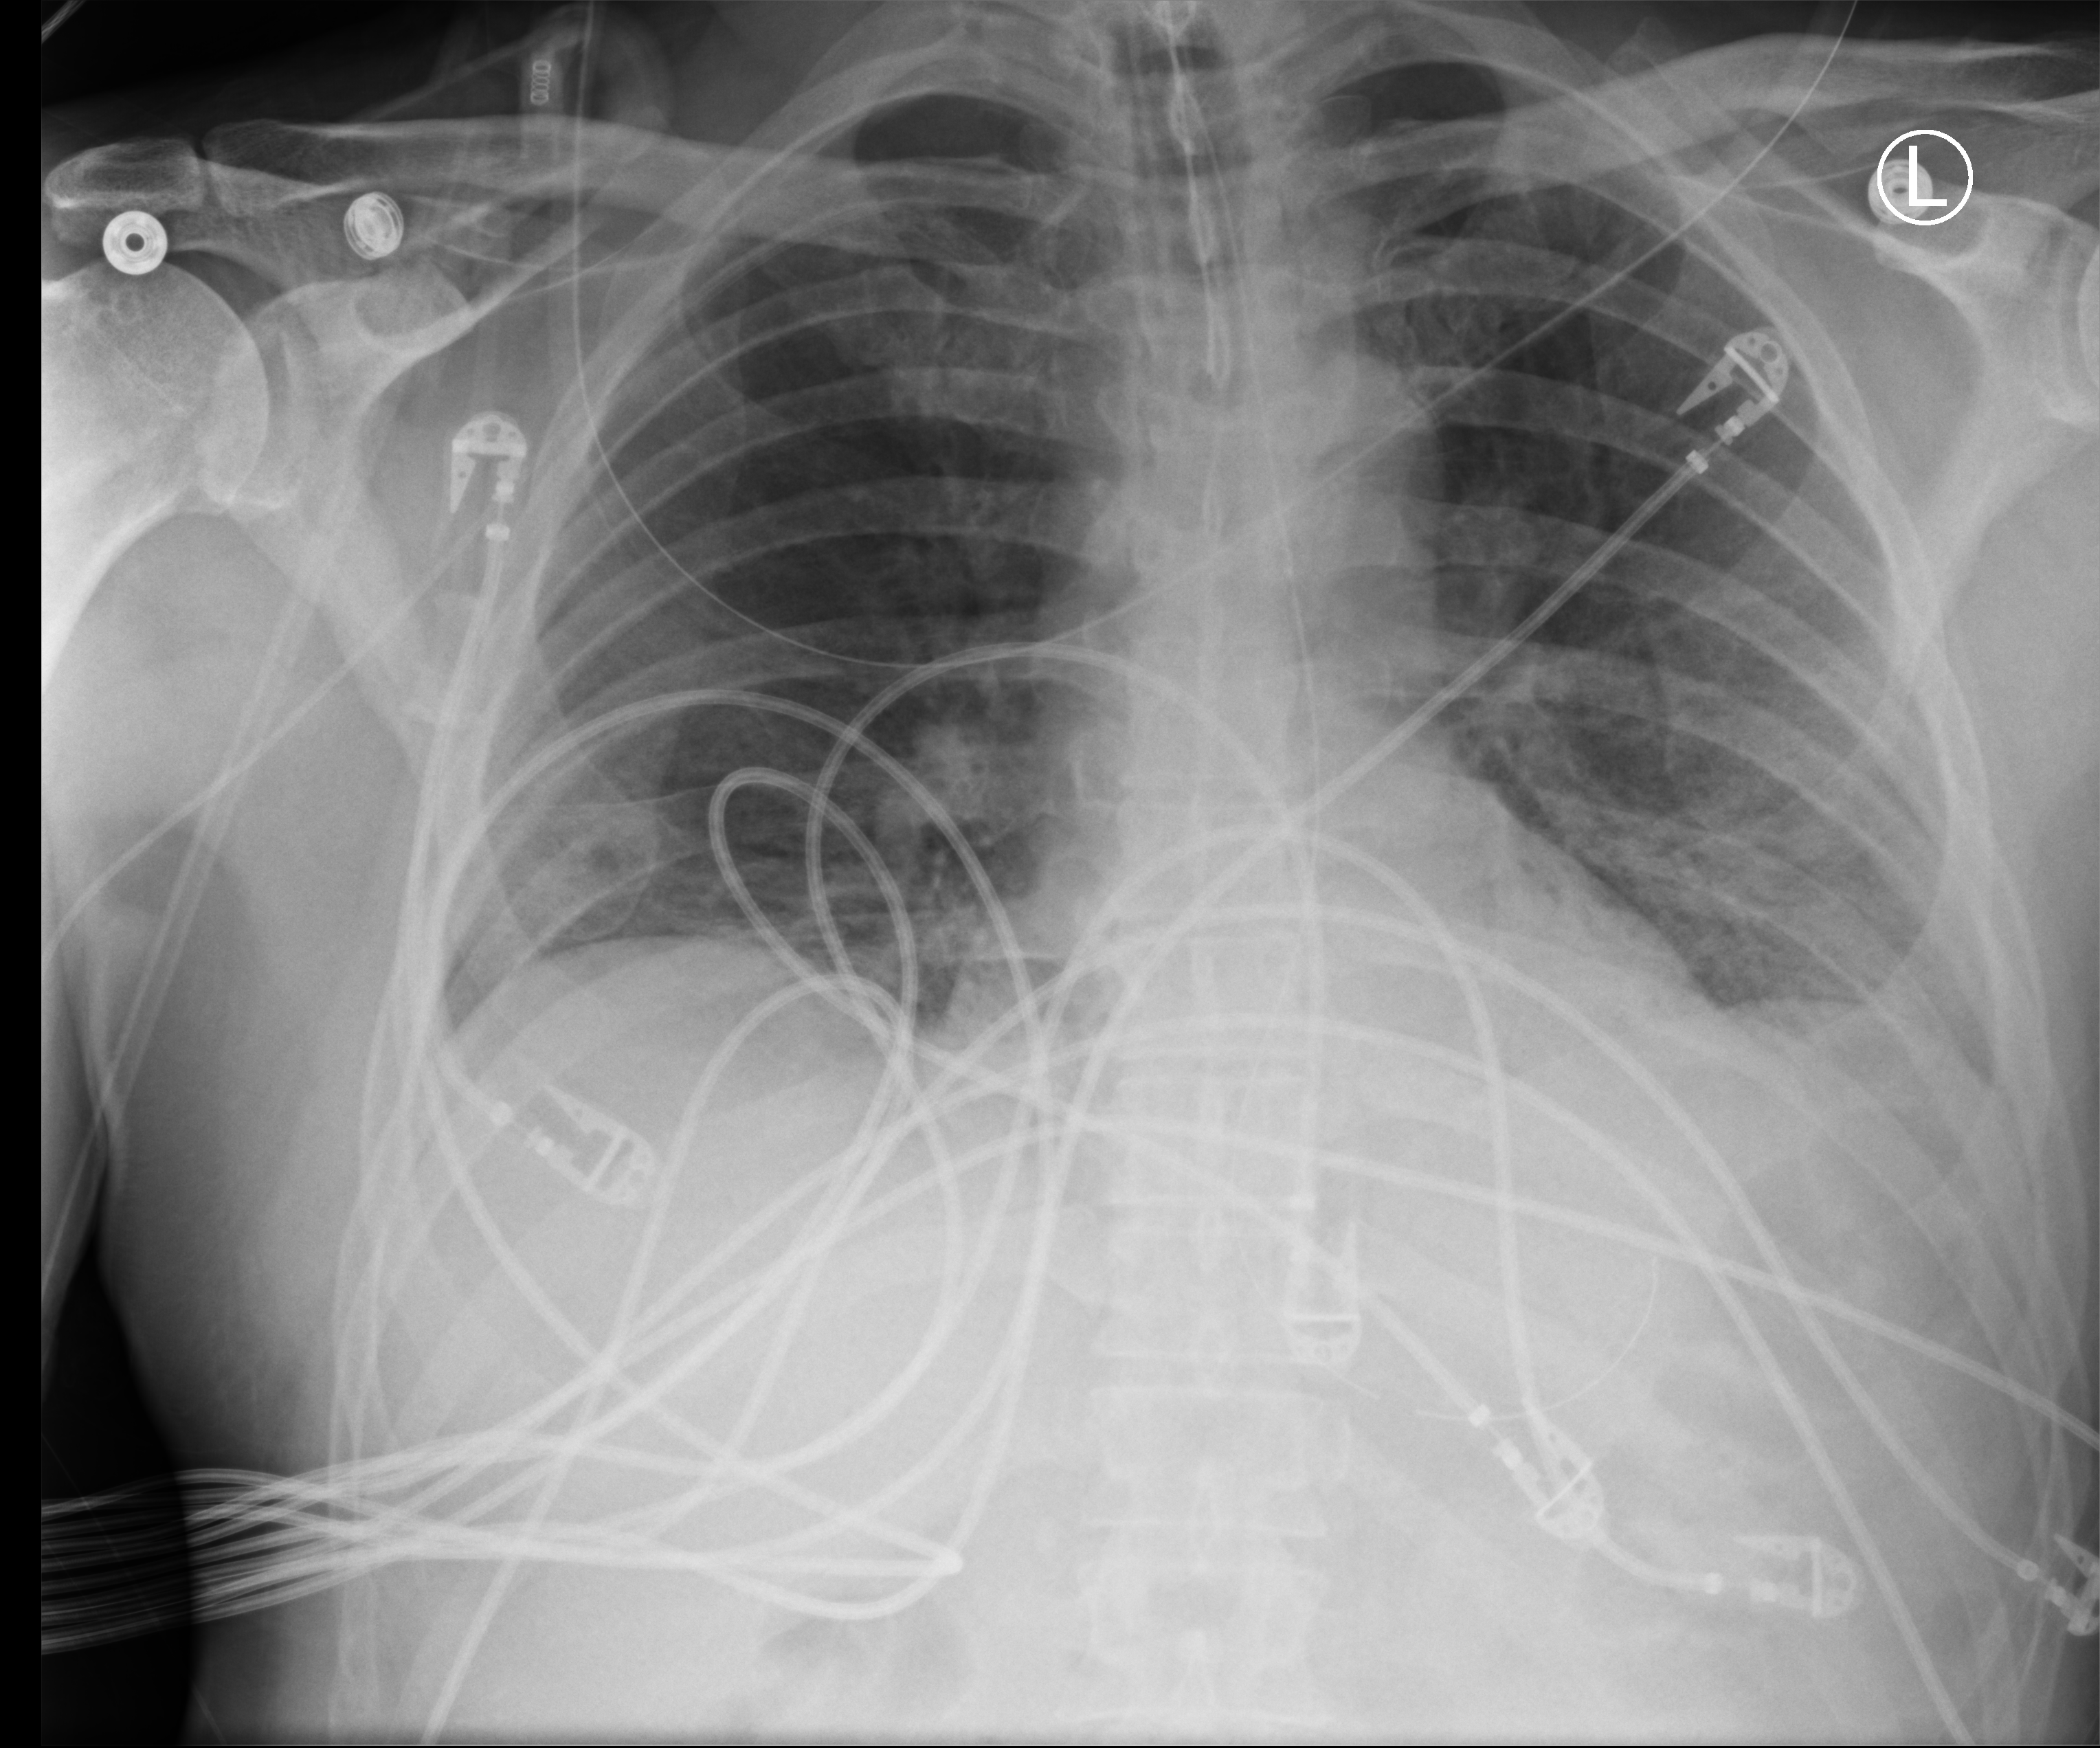
Bedside chest radiograph (computed radiography); anteroposterior (AP) projection. Male patient hospitalised with COVID-19, age 60–74 years.
Admission-level facts for this patient (not findings on this image; timing relative to this image not recorded): mechanically ventilated during this hospital stay: yes.